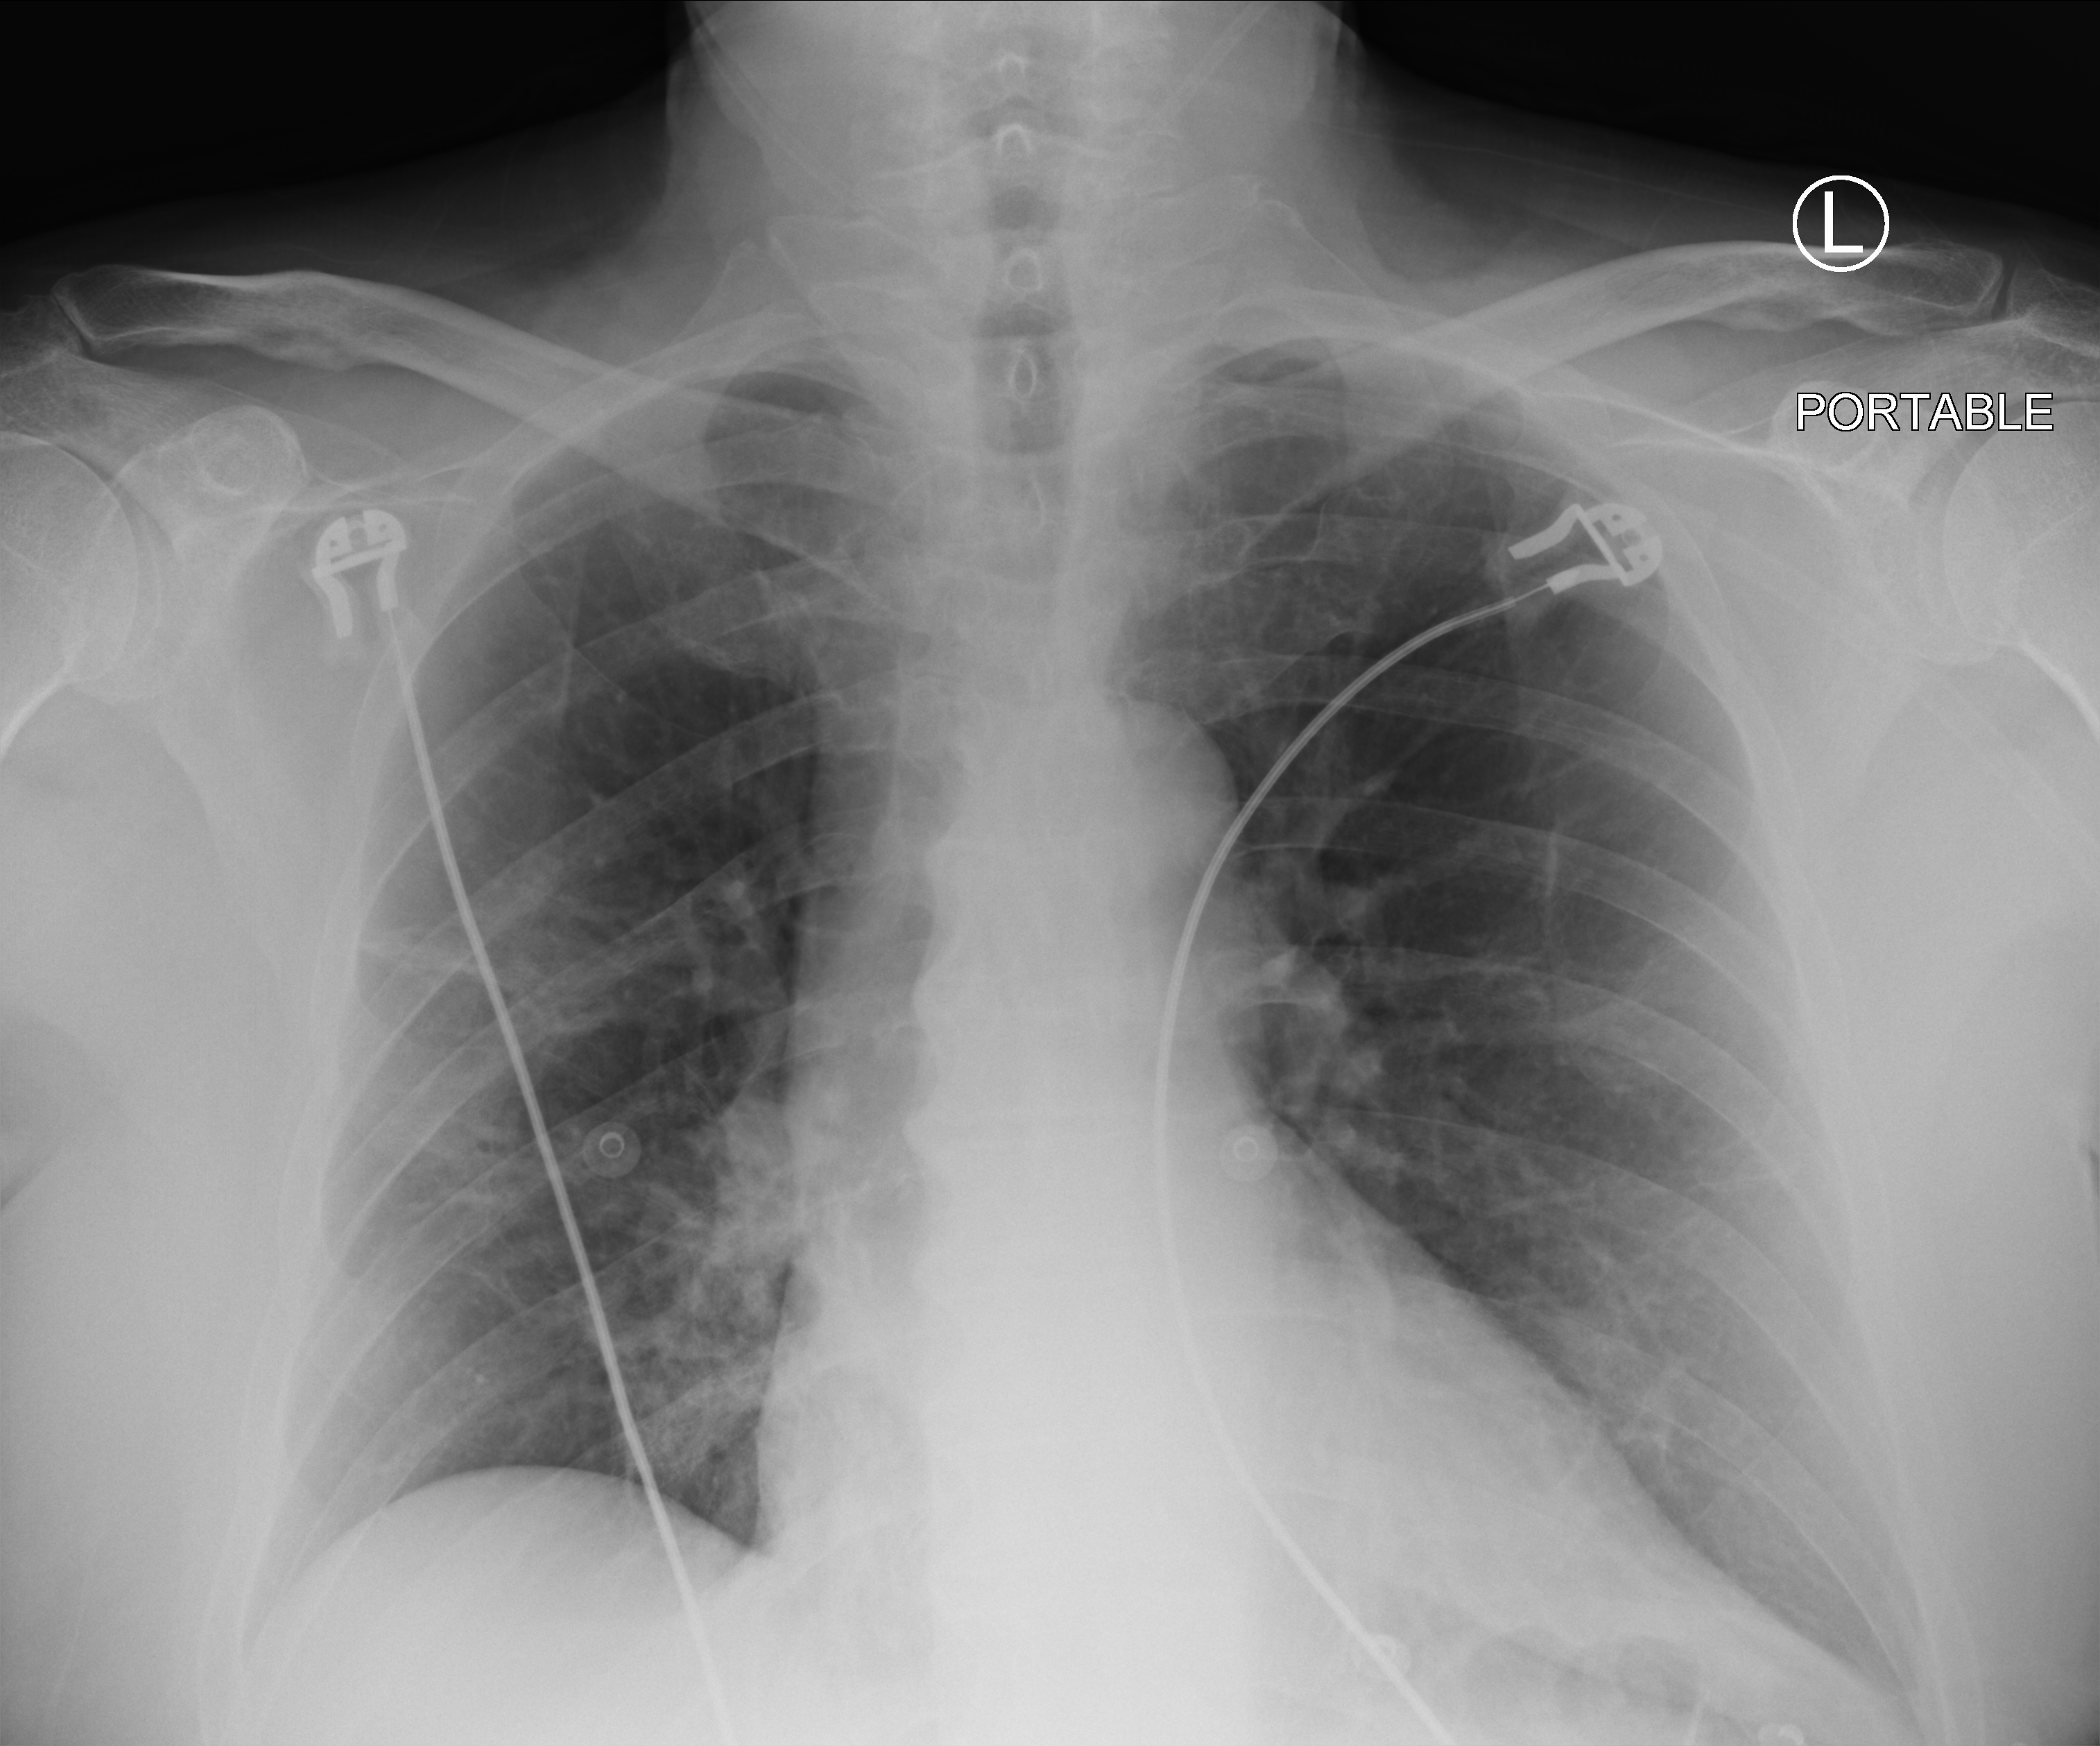
Chest X-ray (portable); anteroposterior (AP) projection. Patient hospitalised with COVID-19; male, aged 60–74 years.
From the hospital-stay record, not from the radiograph (when in the stay this image was taken is not recorded): diabetes (admission record): no; chronic kidney disease (admission record): no; COPD (admission record): no.